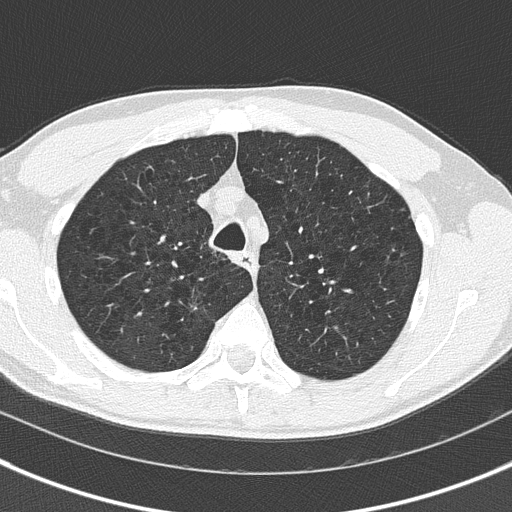
Axial slice from a low-dose chest CT screening exam. First (baseline) screen. Lung window (W 1500 / L -600 HU). Lung (sharp) reconstruction kernel (B50f). 120 kVp. 512 × 512 image matrix, field of view 306 × 306 mm. Male, age 56 years at enrolment. Current smoker at enrolment.
Expert reader's lesion annotation, bounding box <176,292,226,334> (left, top, right, bottom; pixels). The screening reader recorded 3 non-calcified nodules or masses ≥4 mm on this exam; which of them this box marks is not recorded. Official screen result: positive, change unspecified: nodule(s) >= 4 mm or enlarging nodule(s), mass(es), or other non-specific abnormalities suspicious for lung cancer.